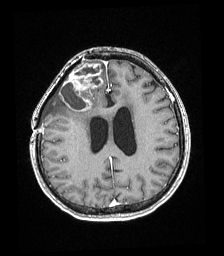
Brain MRI from a brain-tumour surgery series, one axial slice. Slice 75 of 192 in the series (ordered by position). T1-weighted post-contrast. 1 mm slice thickness. 224 × 256 image matrix, field of view 219 × 250 mm. Case-level facts recorded for this patient, not image findings: histopathology: Astrocytoma; WHO grade: 4; IDH mutation: yes.
Outlined on this slice (outlined manually by an expert reader):
- tumour: bounding box [x1, y1, x2, y2] px = [59, 62, 103, 112]